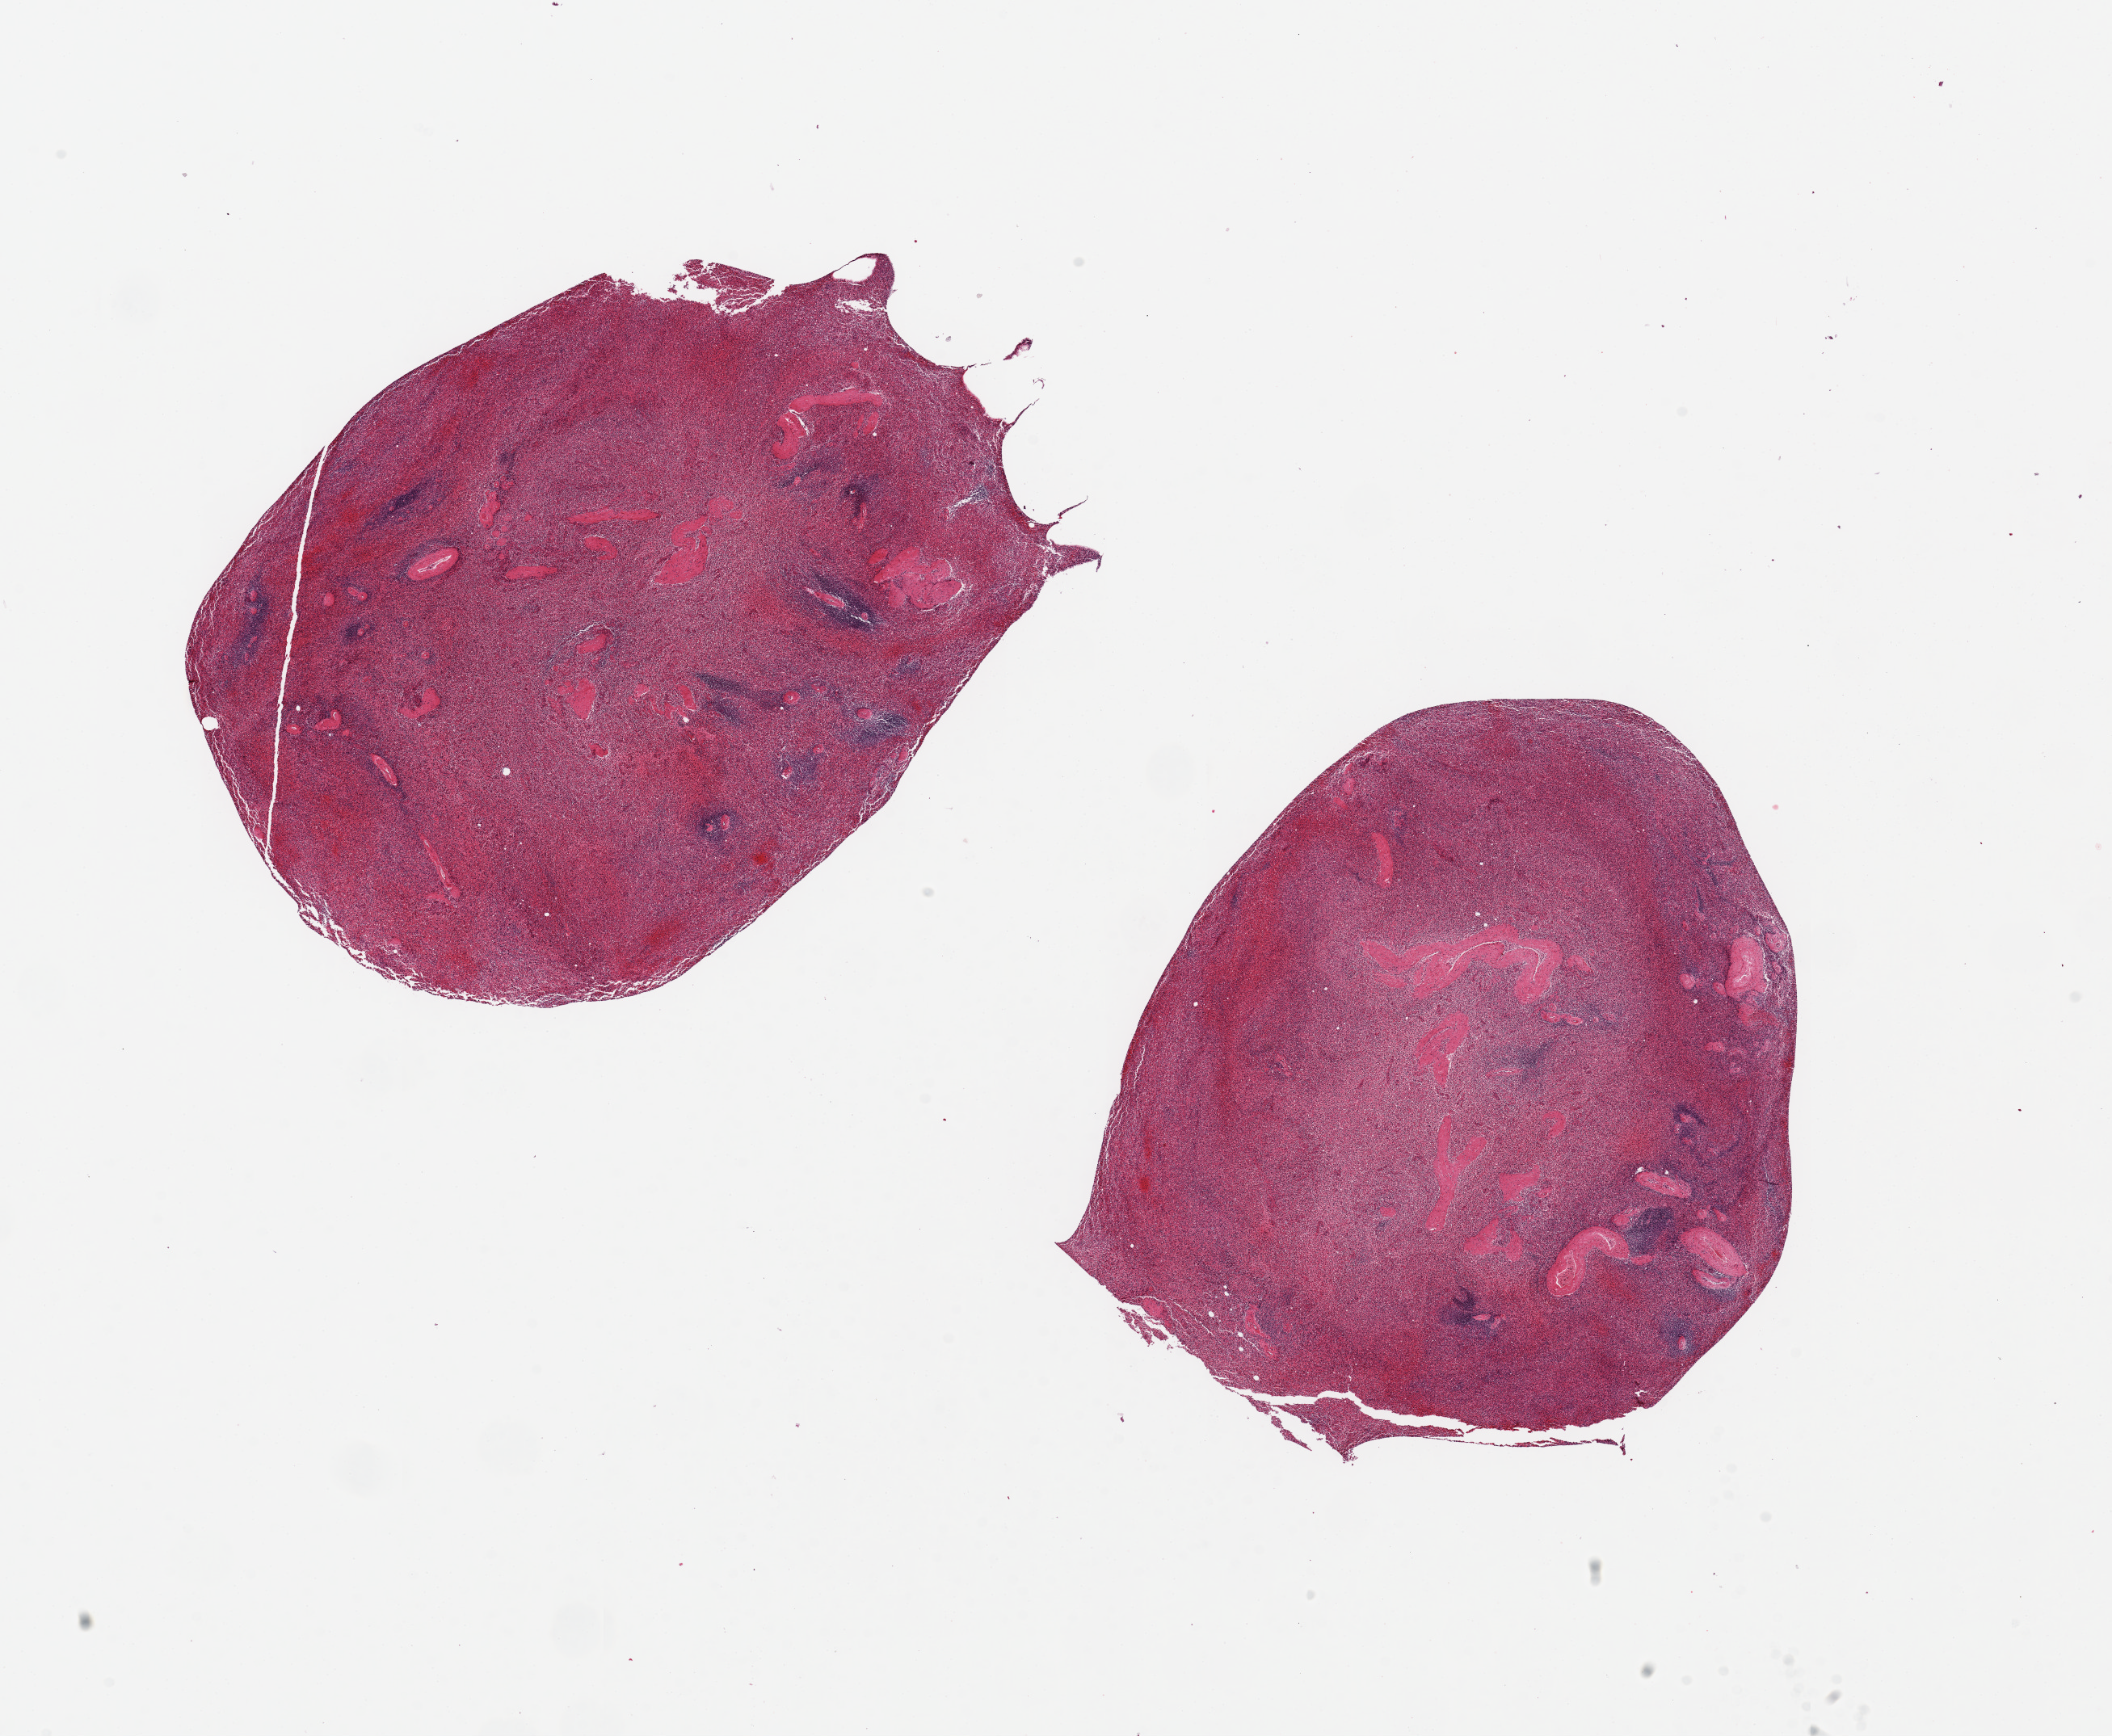
Digitized H&E-stained section, shown as a low-resolution overview of the whole scanned area (about 20.7 x 17.0 mm, slide scanned at 20x); PAXgene-fixed, paraffin-embedded tissue; section of spleen (target tissue); tissue donor sample. Male donor.
• pathologist's review note for this sample: 2 pieces, 6x7 & 8x6mm; moderate congestion